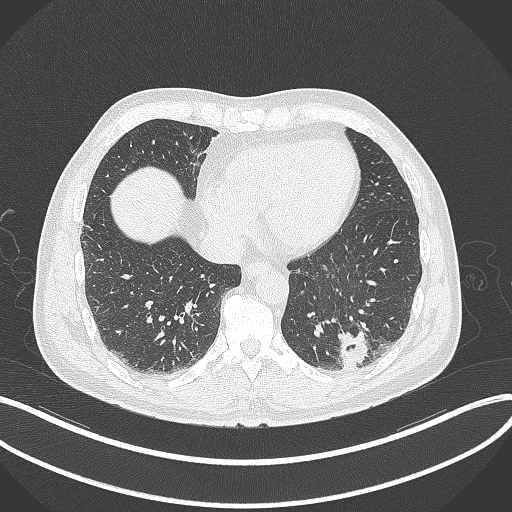
Chest CT, one axial slice; position 83 of 300 along the scan axis; reconstruction kernel B70f; lung window (W 1500 / L -600 HU); 1 mm slice thickness; 512 × 512 image matrix. Male patient, age 54 years. Case-level facts recorded for this patient, not image findings: clinical TNM (as recorded): T1c N0 M1.
Outlined on this slice (rectangle marked by the reading radiologist):
- lung tumour (recorded histology: adenocarcinoma): bounding box <332,328,376,372> (left, top, right, bottom; pixels)